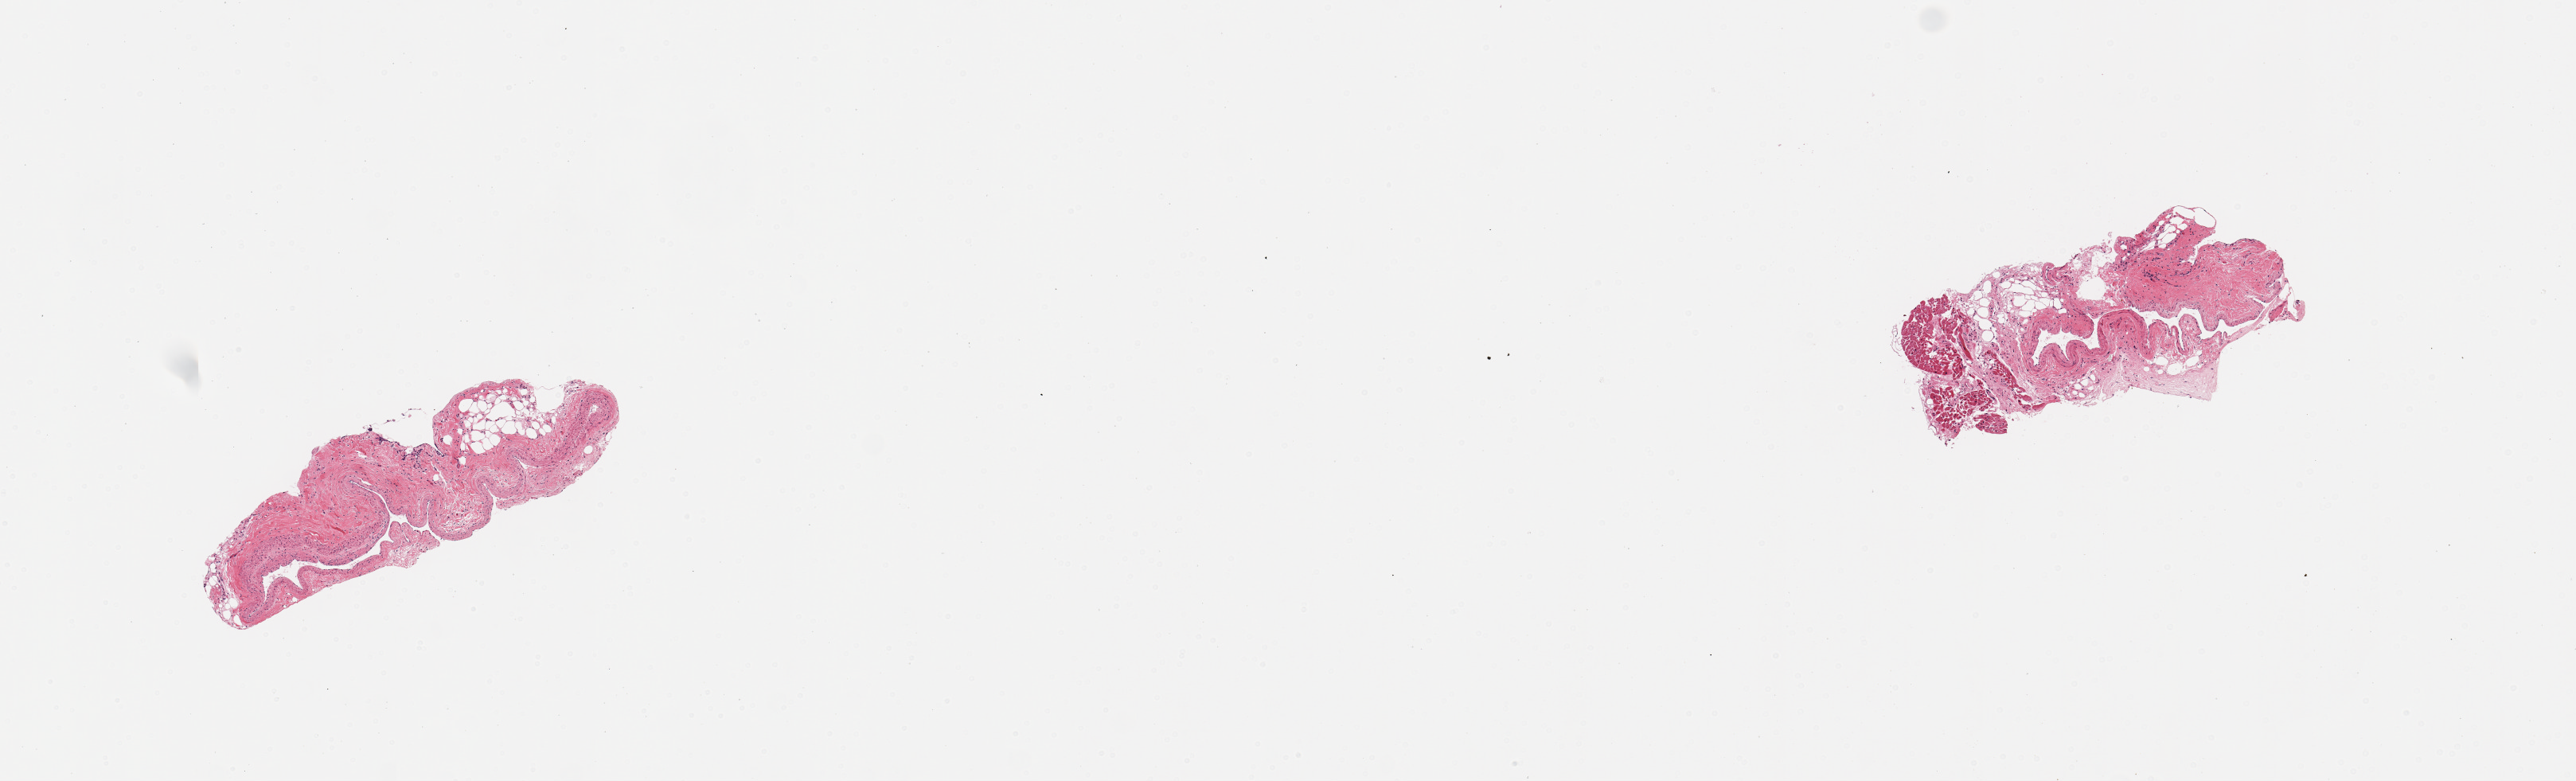
Hematoxylin and eosin (H&E) whole-slide image, brightfield, whole scanned area (about 12.8 x 3.9 mm) shown as a low-resolution overview. PAXgene-fixed, paraffin-embedded tissue. Sampled site (target tissue): coronary artery. Tissue donor sample.
Pathologist's review note for this sample: 2 pieces: 1 small artery, 1 small vein & cardiac muscle.